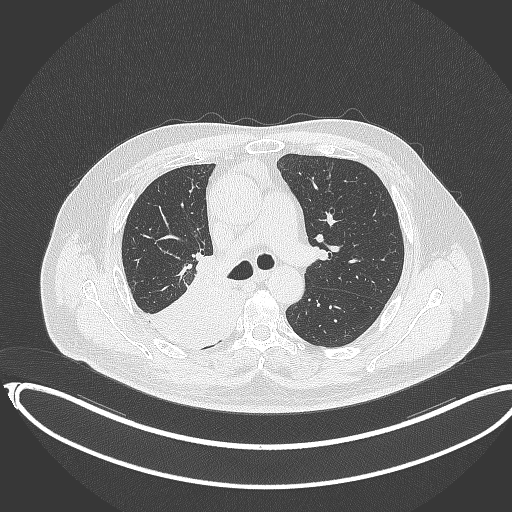
Chest CT, one axial slice; position 231 of 403 along the scan axis; lung window (W 1500 / L -600 HU); 1 mm slice thickness; 512 × 512 image matrix. Patient: male, 68 years. Case-level facts recorded for this patient, not image findings: clinical TNM (as recorded): T2a N0 M0.
Outlined on this slice (bounding box drawn by a radiologist):
- lung tumour (recorded histology: adenocarcinoma): bounding box (x1, y1, x2, y2) in pixels: (140, 257, 228, 345)